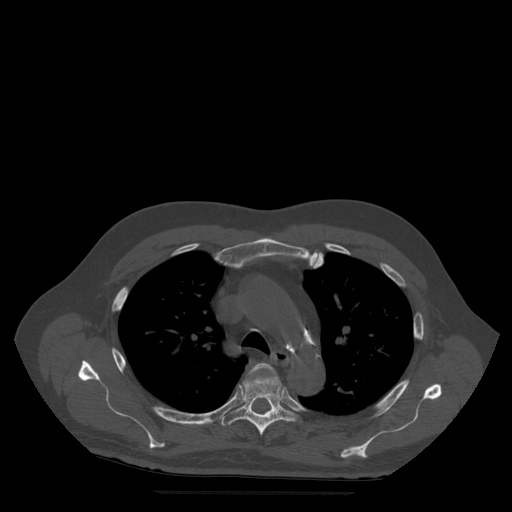
CT including the spine, one axial slice. Slice 376 of 522 in the series (ordered by position). Bone window (W 1800 / L 400 HU). 512 × 512 image matrix, field of view 420 × 420 mm. Patient age 72 years. Case-level facts recorded for this patient, not image findings: primary cancer: prostate.
Structures marked on this image (semi-automatically segmented with operator editing):
- T4 vertebra: bounding box (x1, y1, x2, y2) in pixels: (251, 363, 276, 374)
- T5 vertebra: (222, 369, 299, 436)